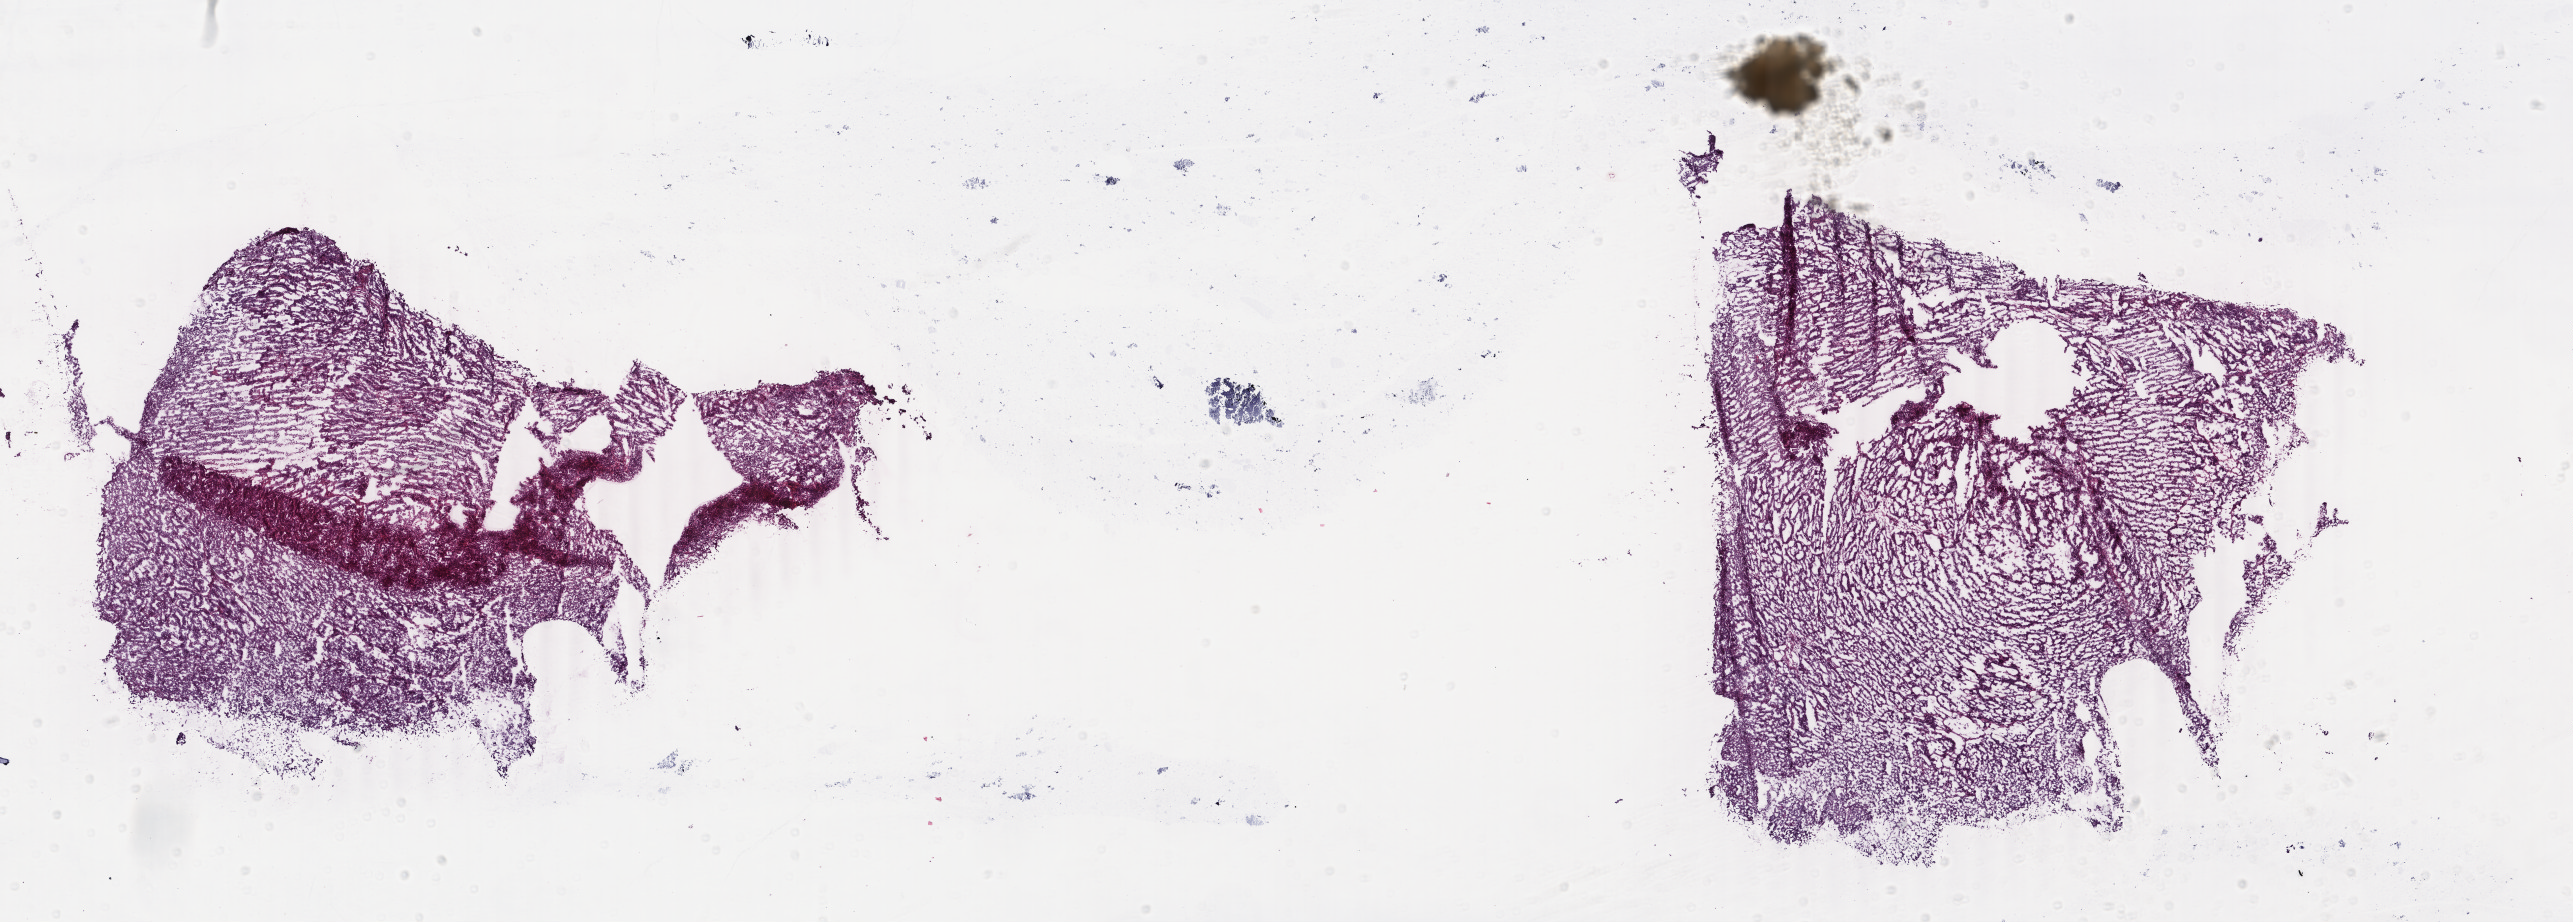
Hematoxylin and eosin (H&E) stained whole-slide image — low-resolution overview of the scanned area, about 20.5 x 7.3 mm (from a 40x scan), frozen section, sample: primary tumour, uterus. Female, age 81 years at initial diagnosis. Histologic grade: G2 (moderately differentiated). Slide review estimates, as recorded: tumour cells 83%, tumour nuclei 92%, normal cells 0%, stromal cells 2%, necrosis 15%. Infiltration values recorded for this section: lymphocyte infiltration 0%, monocyte infiltration 0%, neutrophil infiltration 4%.
Histologic diagnosis: Endometrioid adenocarcinoma, NOS (endometrium). FIGO stage: IIA.